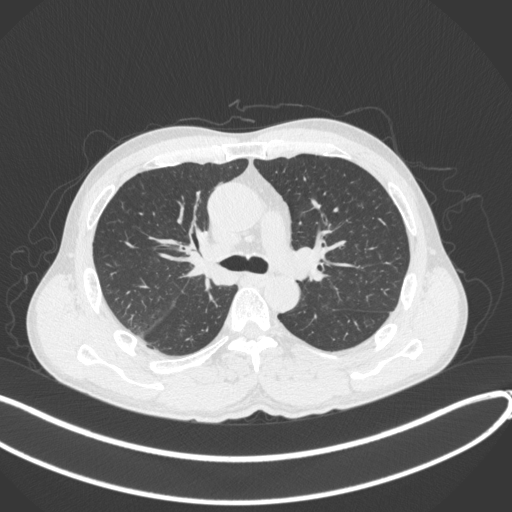
Chest CT, one axial slice. Slice 247 of 409 in the series (ordered by position). Reconstruction kernel B31f. Lung window (W 1500 / L -600 HU). 1 mm slice thickness. 512 × 512 image matrix, field of view 400 × 400 mm. Patient: male, 53 years. From the clinical record (not read from this slice): clinical TNM (as recorded): T1b N0 M0.
Structures marked on this image (rectangle marked by the reading radiologist):
- lung tumour (recorded histology: squamous cell carcinoma): bounding box [x1, y1, x2, y2] px = [176, 218, 234, 289]